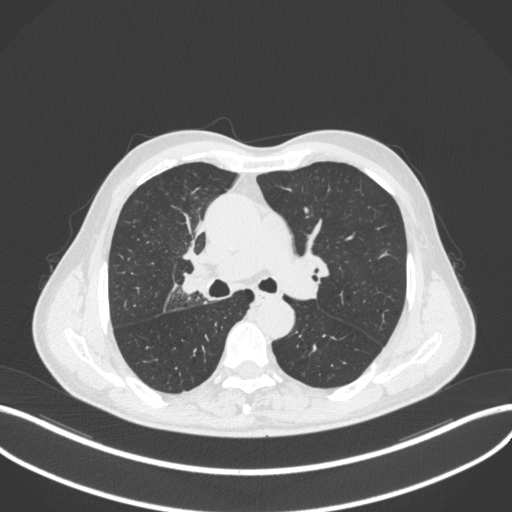
Chest CT, one axial slice. Slice 299 of 490 in the series (ordered by position). Reconstruction kernel B31f. 120 kVp. Lung window (W 1500 / L -600 HU). 1 mm slice thickness. 512 × 512 image matrix, field of view 400 × 400 mm. Patient: male, 69 years. Case-level facts recorded for this patient, not image findings: clinical TNM (as recorded): T2a N0 M0.
Outlined on this slice (rectangle marked by the reading radiologist):
- lung tumour (recorded histology: adenocarcinoma): bounding box <180,264,210,300> (left, top, right, bottom; pixels)